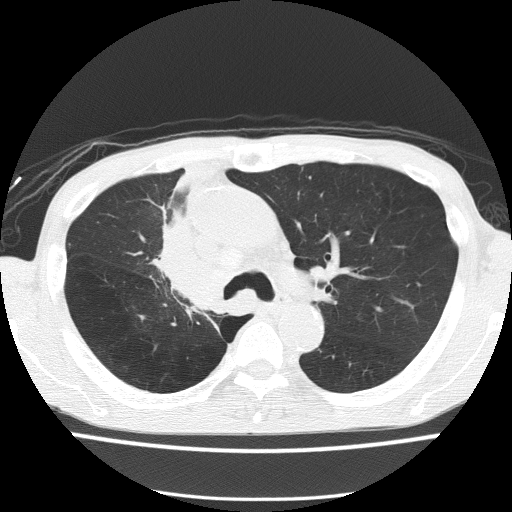
Low-dose screening chest CT, one axial slice. Position 100 of 150 along the scan axis. Reconstruction kernel FC51. Lung window (W 1500 / L -600 HU). 2 mm slice thickness. 512 × 512 image matrix.
Outlined on this slice (outlined manually by an expert reader):
- lesion 1 (tumor, hilum of right lung): bounding box [x1, y1, x2, y2] px = [164, 219, 225, 310]